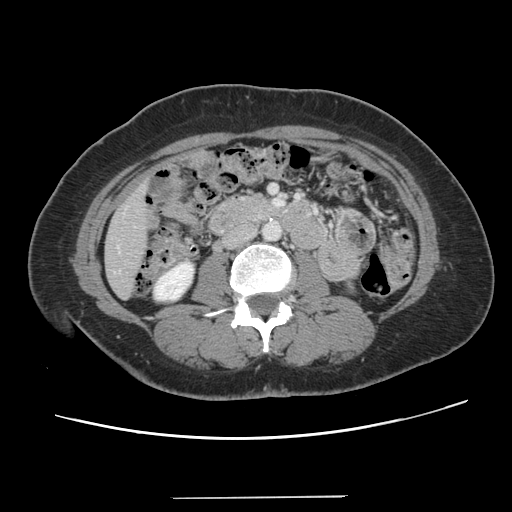
Contrast-enhanced abdominal CT, one axial slice. Position 32 of 141 along the scan axis. Soft-tissue window (W 400 / L 40 HU). 512 × 512 image matrix, field of view 366 × 366 mm. Female patient, age 53 years. Case-level facts recorded for this patient, not image findings: diagnosis: colorectal cancer liver metastases, imaged before liver resection; multiple liver metastases: no; largest metastasis: 14.5 cm; disease in both lobes: yes.
Outlined on this slice (expert manual segmentation):
- liver: bounding box (x1, y1, x2, y2) in pixels: (106, 188, 148, 298)
- planned liver remnant (the part of the liver to remain after resection): (106, 208, 148, 297)